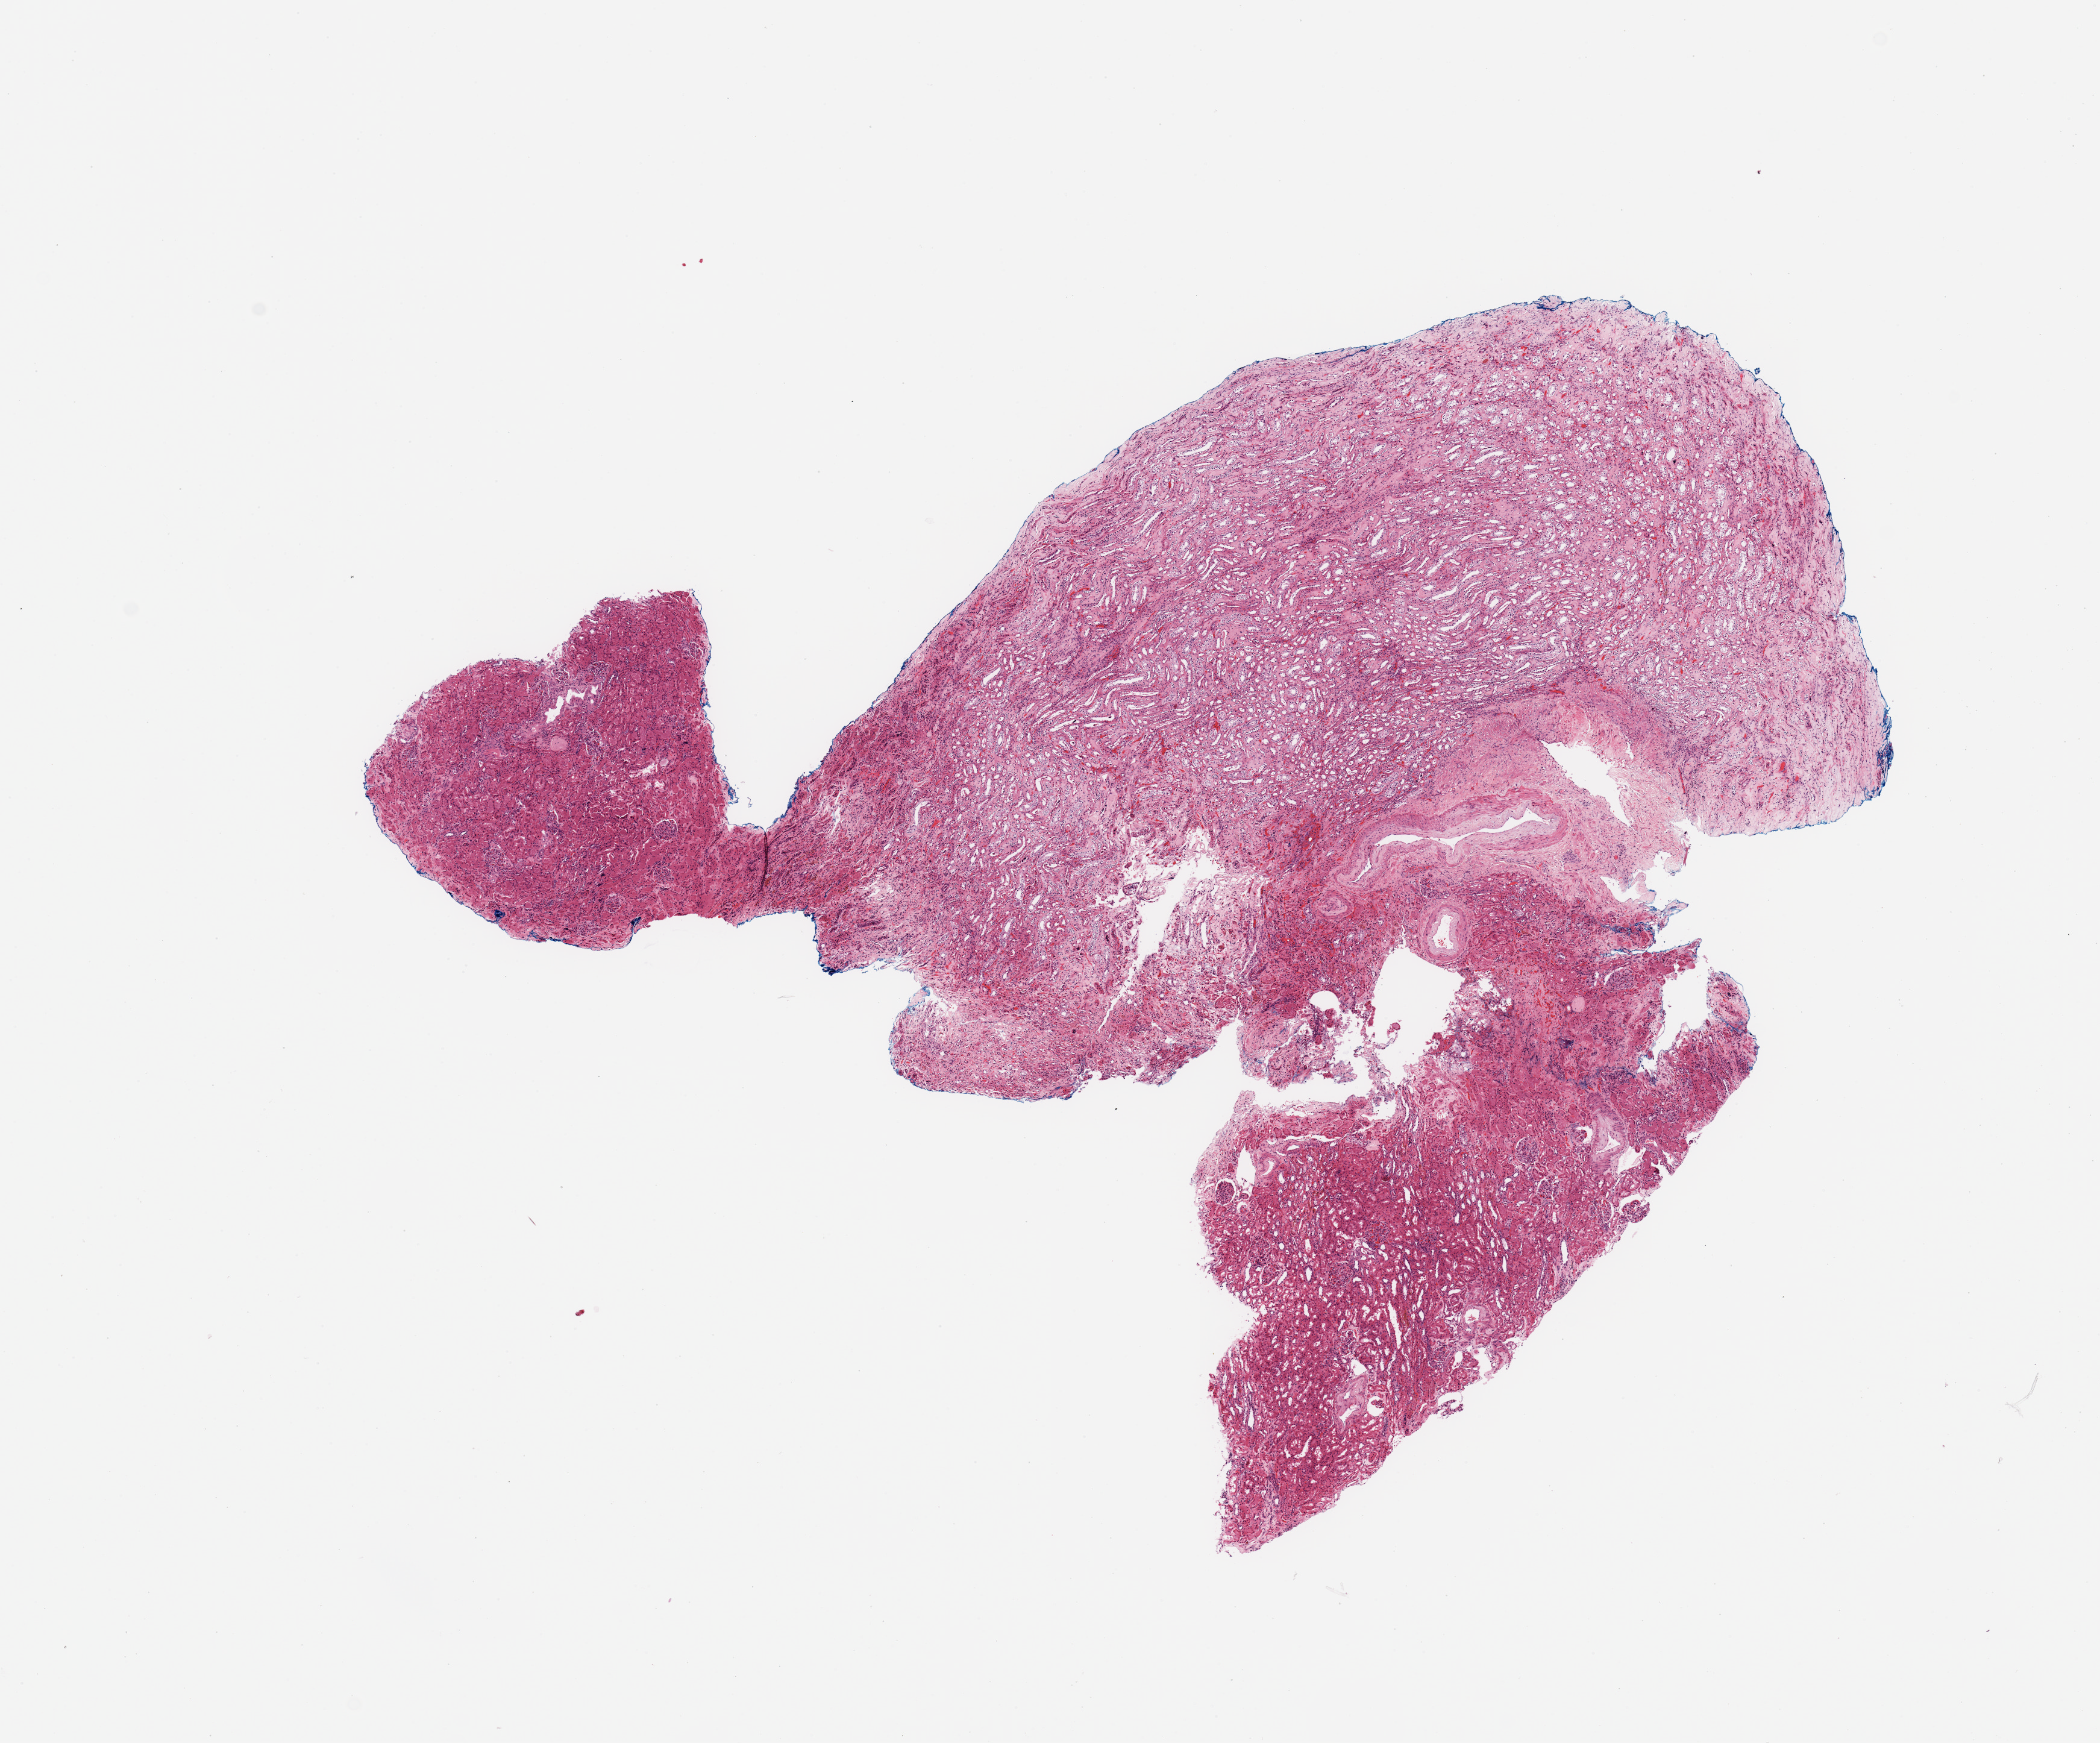
Hematoxylin and eosin (H&E) stained whole-slide image — a low-resolution overview of the entire scanned area, about 13.8 x 11.4 mm (acquisition: 20x scan); normal (non-tumour) tissue sample, sampled site: kidney. Male, 66 y/o.
This section: normal (non-tumour) tissue from the same patient. Patient diagnosis: Renal cell carcinoma, NOS.